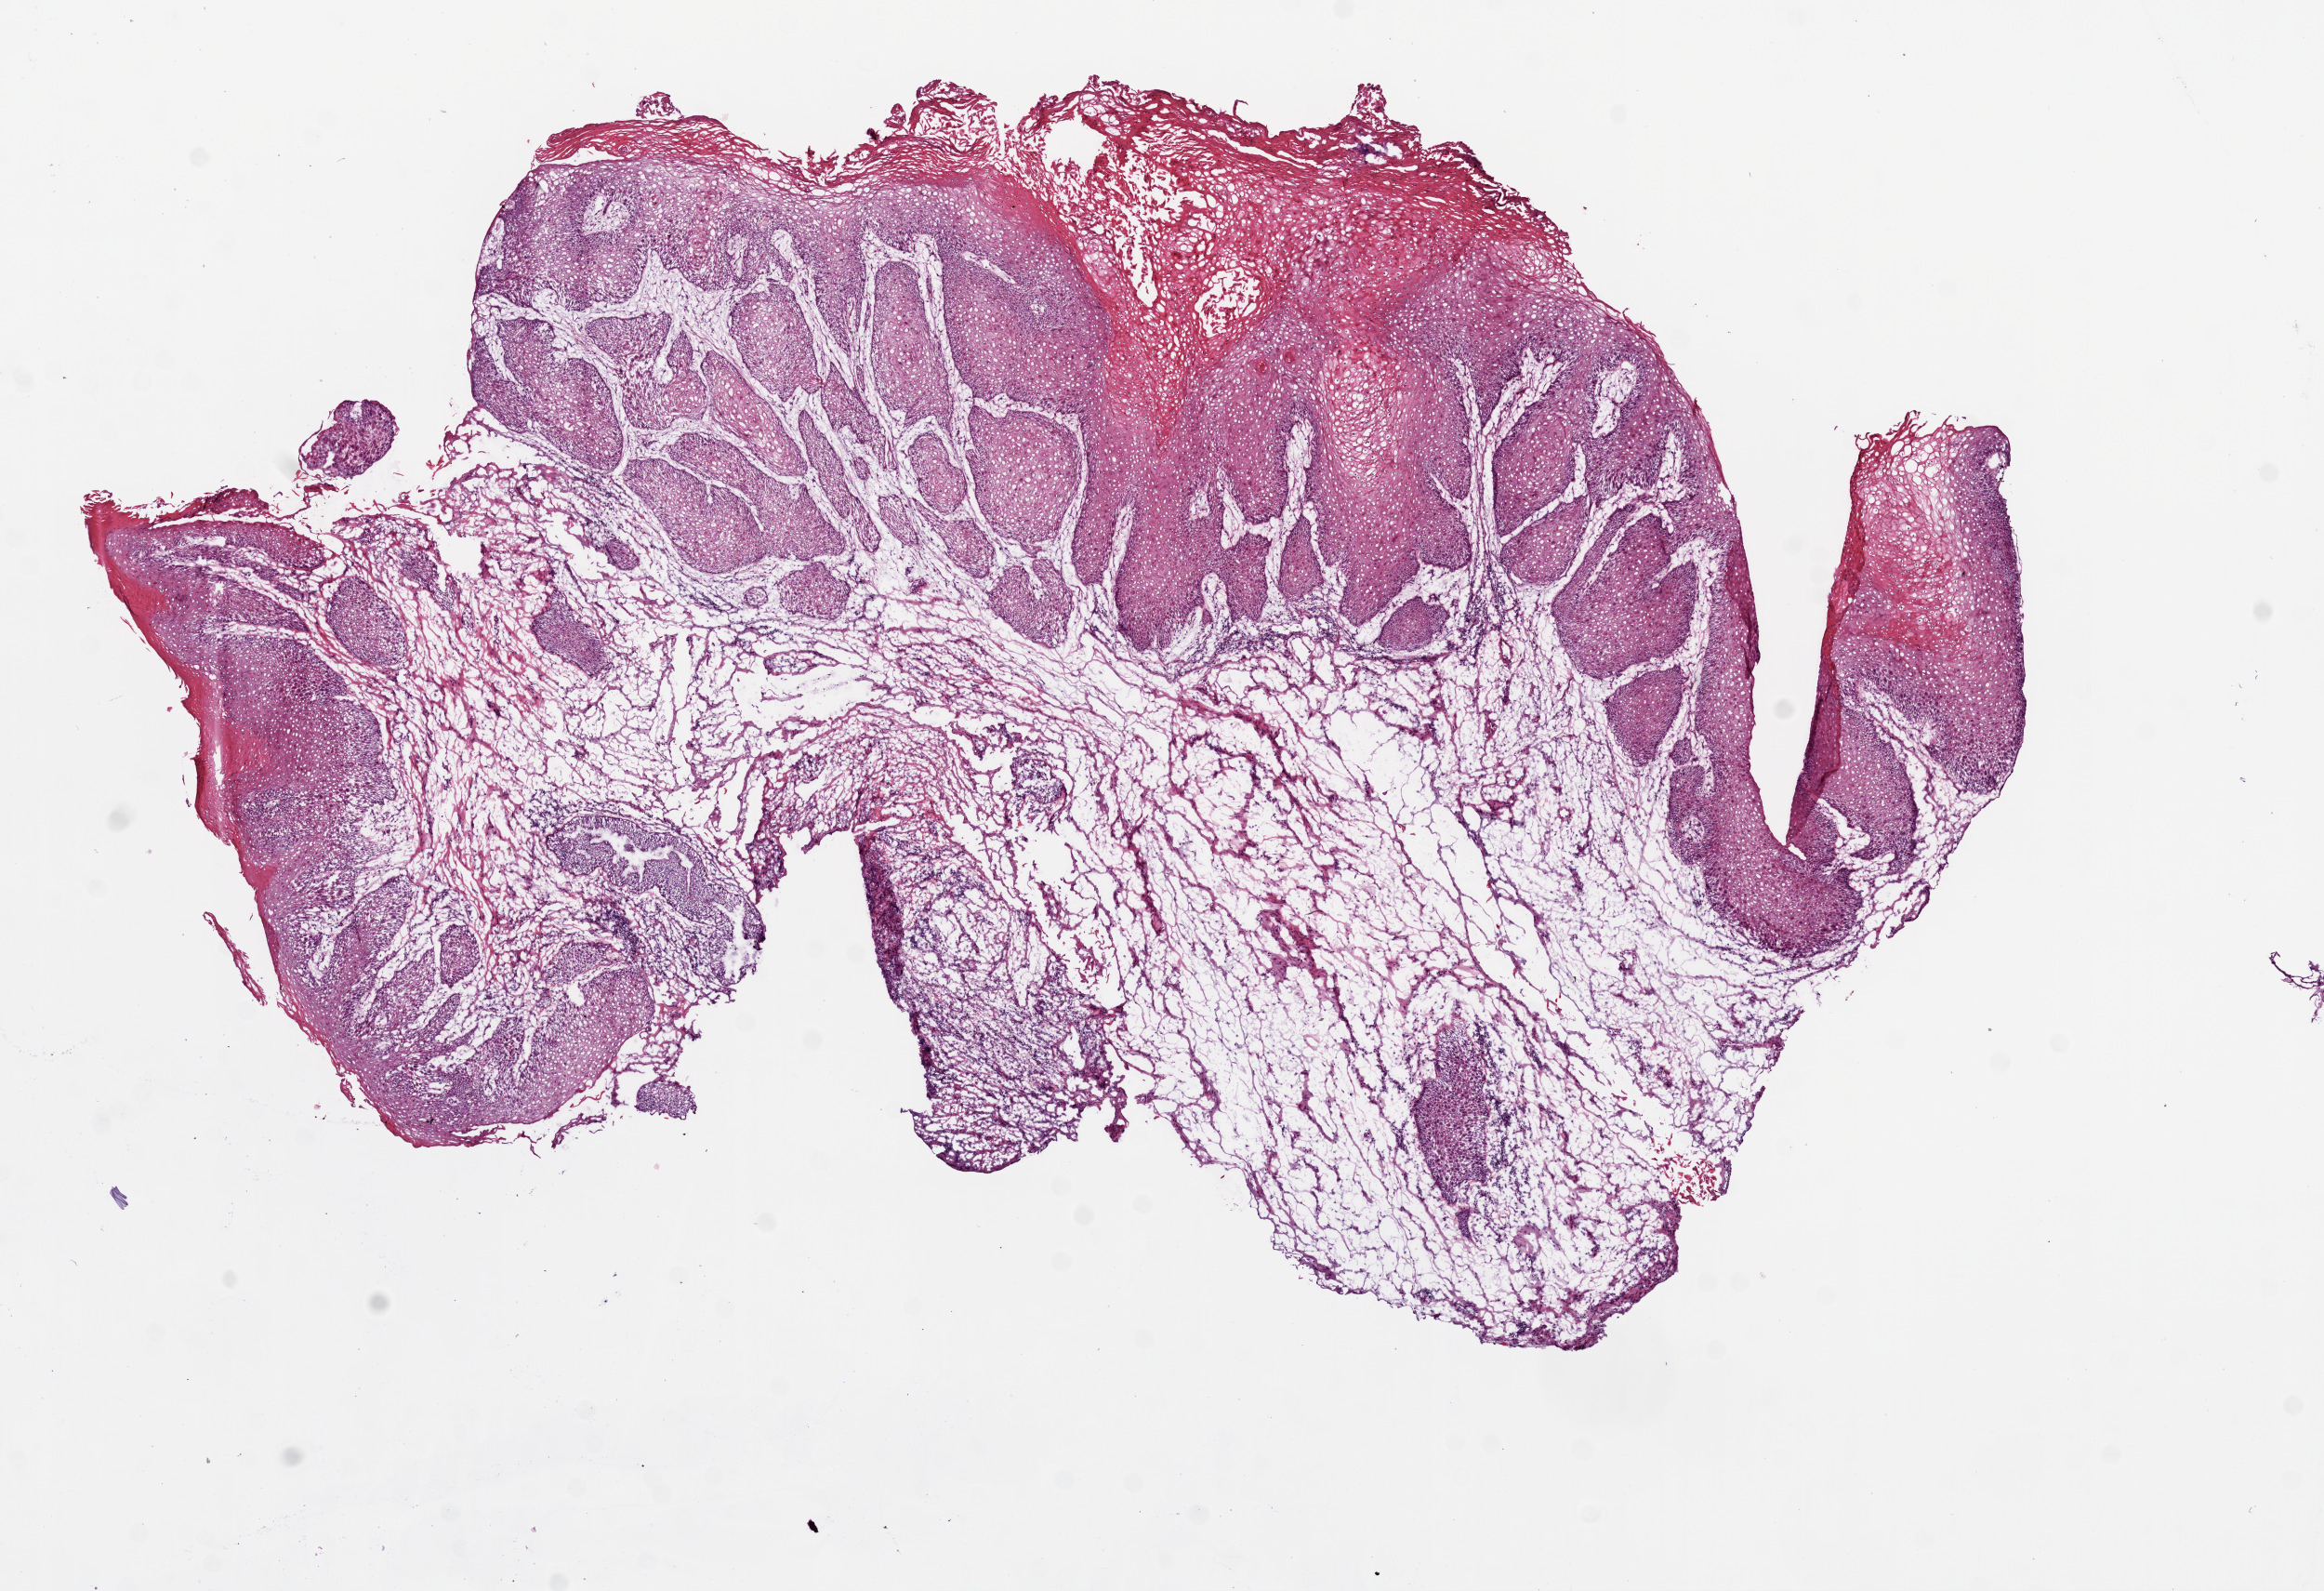
Digitized H&E tissue section (whole slide), a low-resolution overview of the entire scanned area, about 10.0 x 6.9 mm (acquisition: 20x scan); frozen section from the bottom of the tissue portion; sample: primary tumour, head and neck. Patient: female, age at initial diagnosis 61 years. Histologic grade: G1 (well differentiated). Slide review estimates, as recorded: tumour cells 50%, tumour nuclei 80%, normal cells 0%, stromal cells 50%, necrosis 0%.
- AJCC pathologic stage: II
- histologic diagnosis: Squamous cell carcinoma, NOS (larynx, NOS)